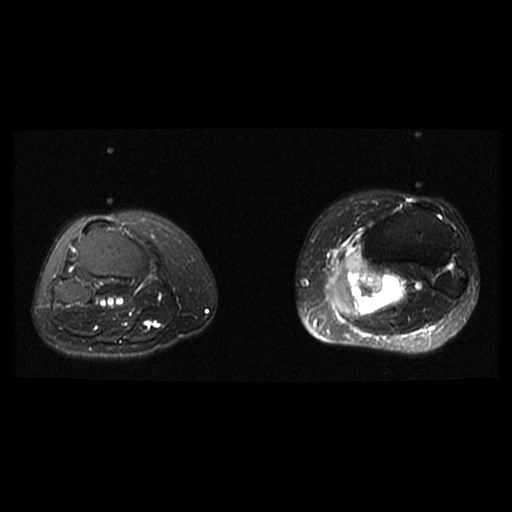
MRI of an extremity soft-tissue mass, one axial slice. T2-weighted fat-saturated. 6 mm slice thickness. 512 × 512 image matrix. Female patient. Case-level facts recorded for this patient, not image findings: histological type: extraskeletal high grade osteogenic sarcoma; grade: high; site of the primary tumour: left calf.
Annotated regions visible in this slice (manually delineated by an expert):
- gross tumour volume (mass): bounding box <326,256,405,315> (left, top, right, bottom; pixels)